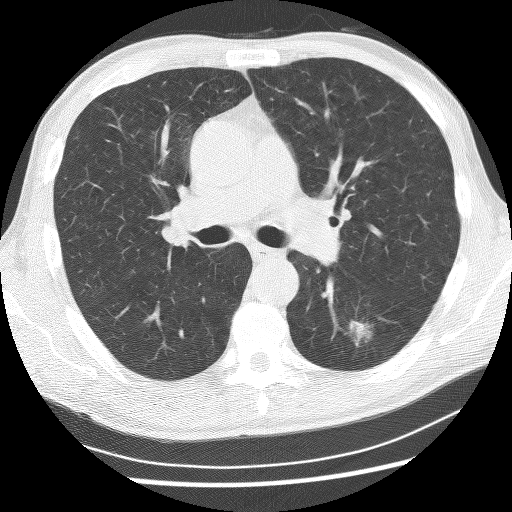
Low-dose screening chest CT, axial slice. Baseline screening round. Lung window (W 1500 / L -600 HU). 2.5 mm slice thickness. Lung (sharp) reconstruction kernel (BONE). Slice 102 of 253 in the series. Male participant, aged 62 years at enrolment. Current smoker at enrolment.
- Expert-annotated lung lesion, box from (x=332, y=309) to (x=380, y=355) px.
- Reader record for this screening exam (exam-level; its link to the box is not recorded): non-calcified nodule or mass ≥4 mm, left lower lobe, 21 × 17 mm, spiculated (stellate) margins, soft tissue attenuation.
- Lung cancer was diagnosed 58 days after this screen: non-small cell carcinoma, left lower lobe, poorly differentiated (G3), stage IA (AJCC 6th edition), 11 mm at pathology.